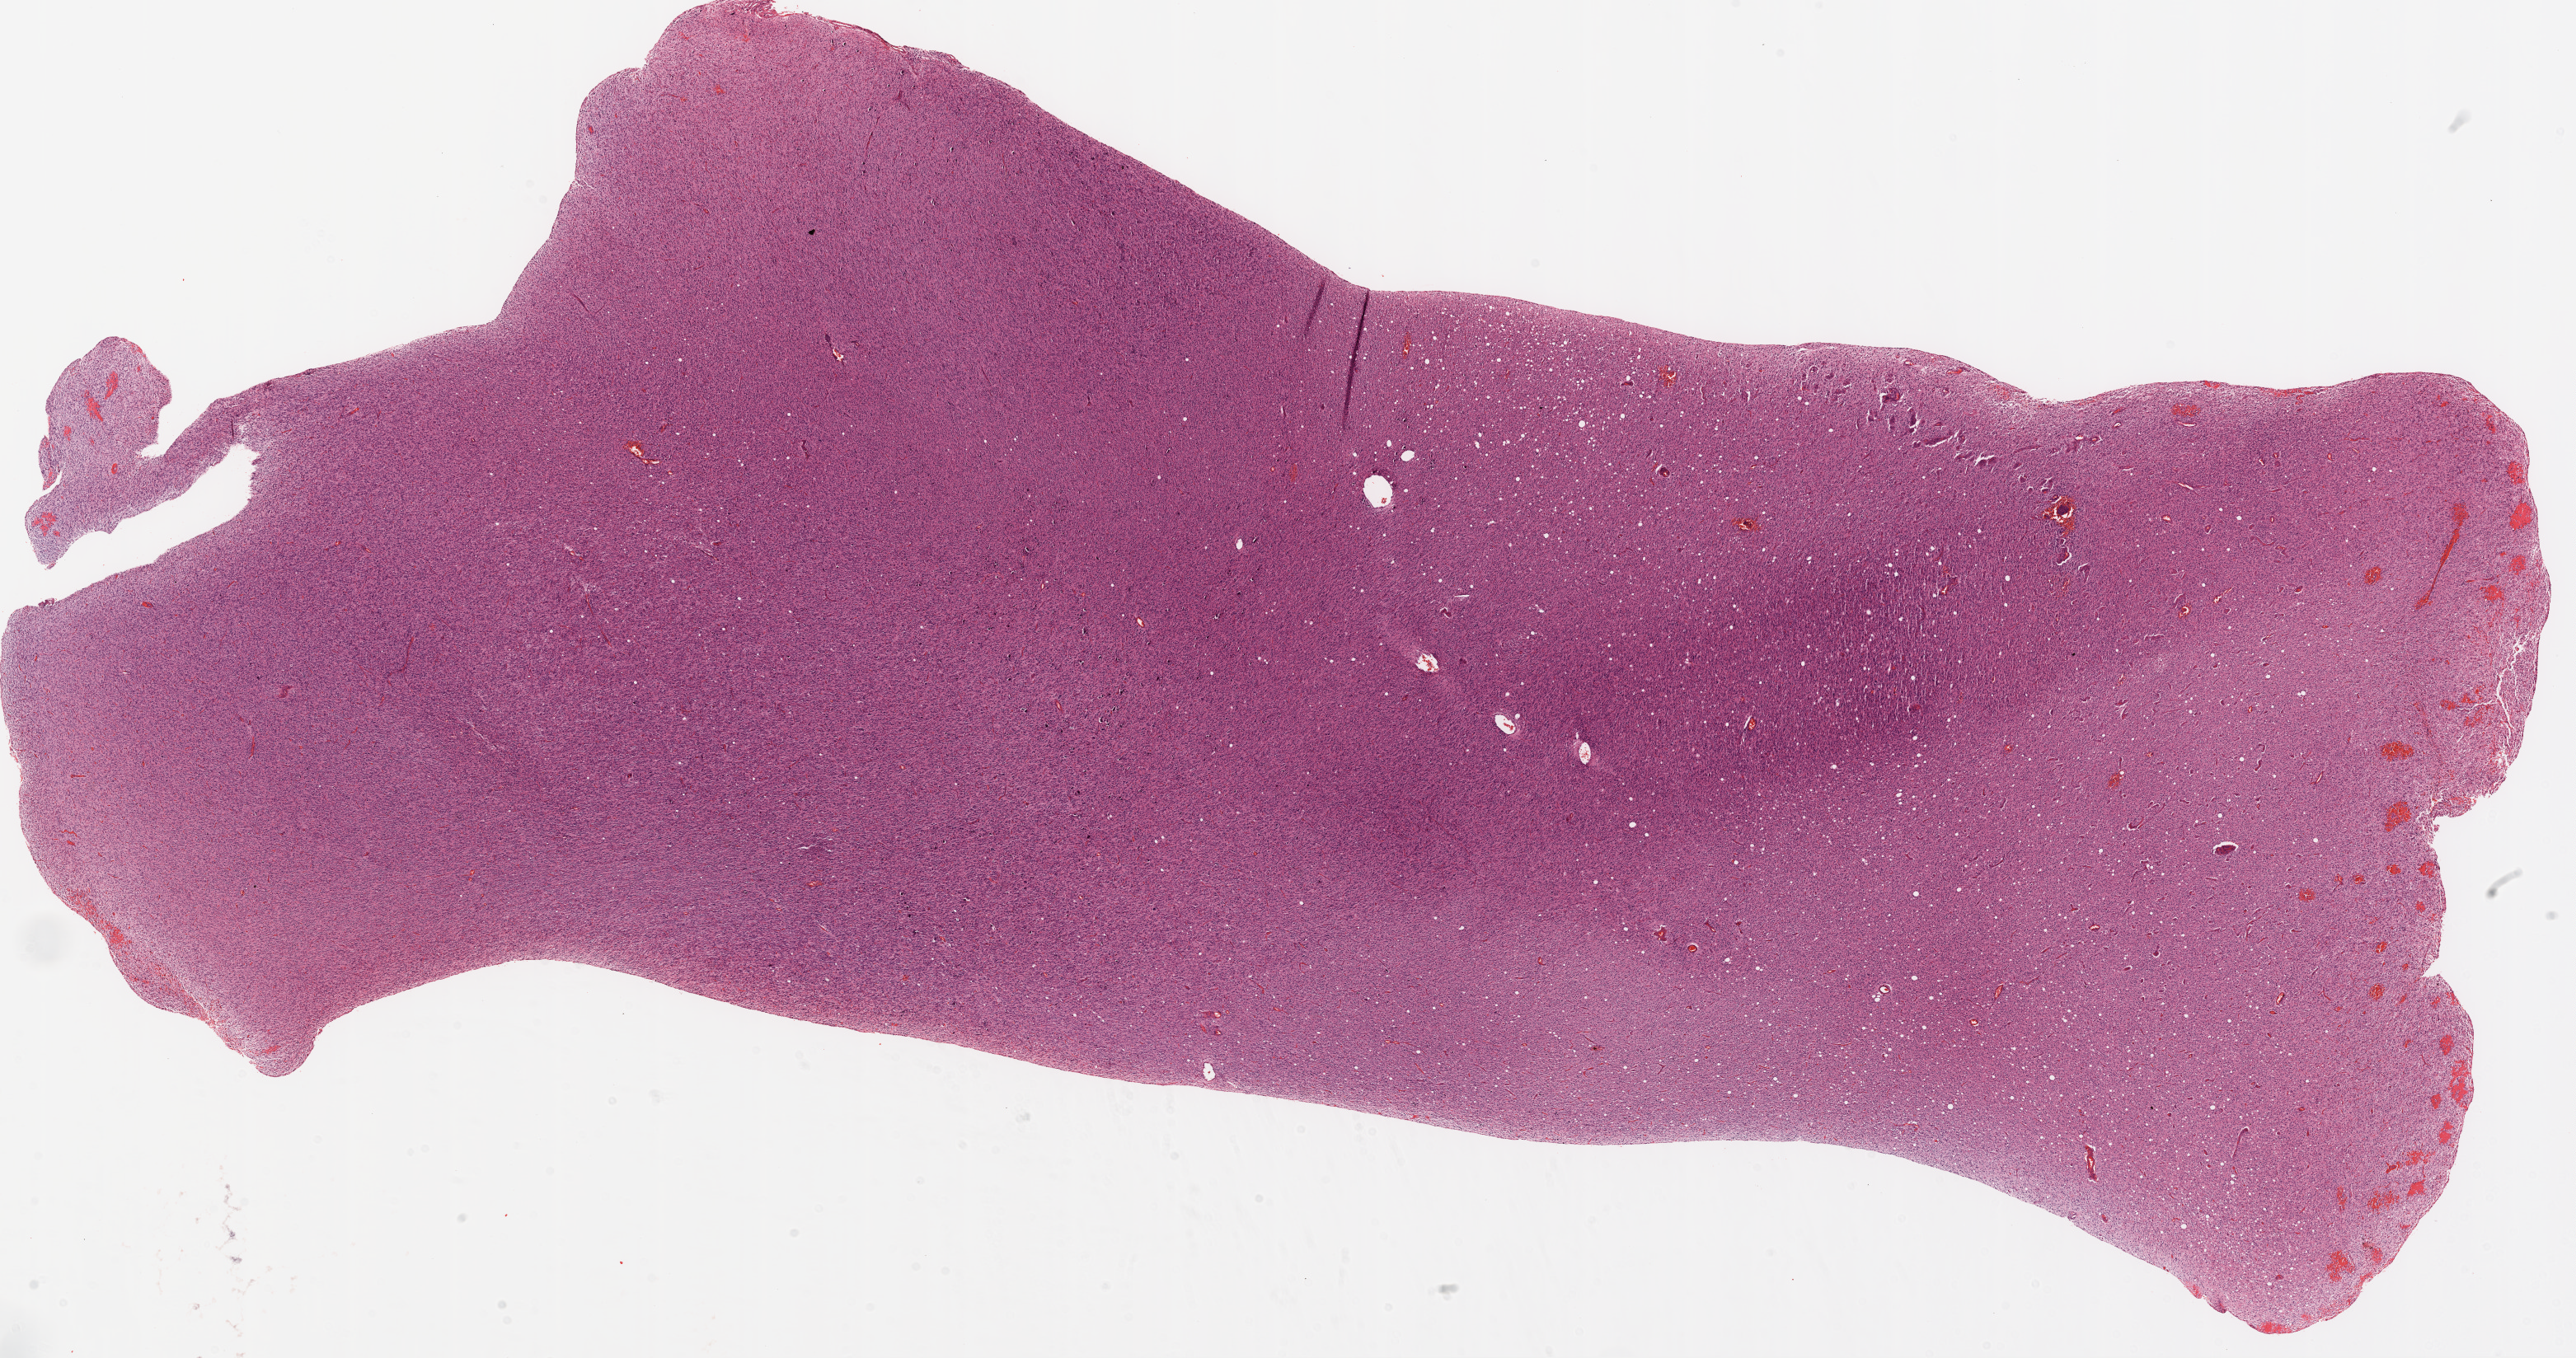
Hematoxylin and eosin (H&E) stained whole-slide image — low-resolution overview of the scanned area, about 25.1 x 13.2 mm. Formalin-fixed paraffin-embedded (FFPE) diagnostic section. Primary tumour sample from the brain. Male patient; age at initial diagnosis 50 years.
Diagnosis: Glioblastoma.